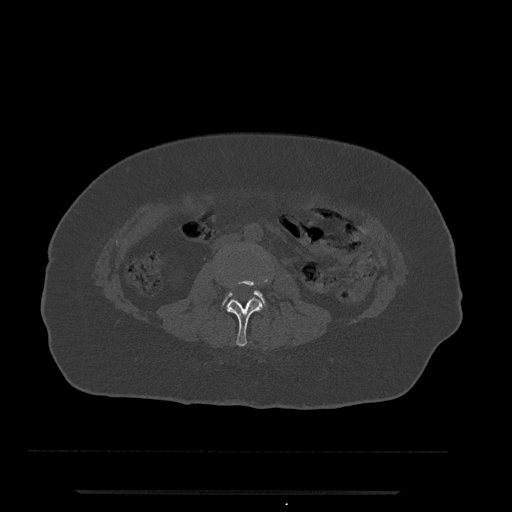
CT including the spine, one axial slice. Slice 9 of 797 in the series (ordered by position). 120 kVp. Bone window (W 1800 / L 400 HU). 0.5 mm slice thickness. 512 × 512 image matrix, field of view 440 × 440 mm. Female patient, age 51 years. Case-level facts recorded for this patient, not image findings: primary cancer: neuro; vertebrae with lytic lesions (as recorded): T8.
Annotated regions visible in this slice (semi-automatically segmented with operator editing):
- L2 vertebra: bounding box <226,276,270,347> (left, top, right, bottom; pixels)